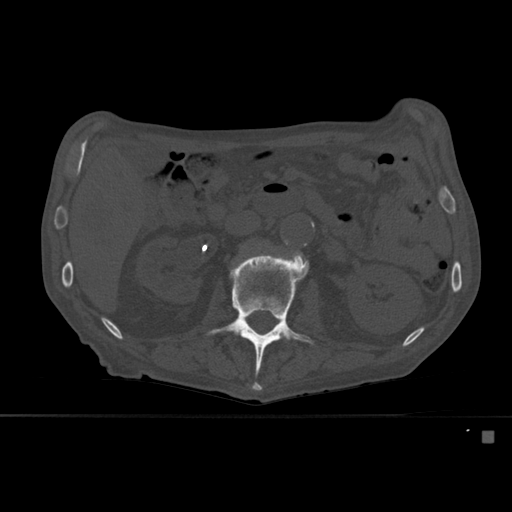
CT including the spine, one axial slice. Position 234 of 527 along the scan axis. Bone window (W 1800 / L 400 HU). 1.5 mm slice thickness. 512 × 512 image matrix, field of view 373 × 373 mm. Patient: male, 78 years. From the clinical record (not read from this slice): primary cancer: prostate.
Annotated regions visible in this slice (semi-automatic segmentation, software-assisted and operator-edited):
- L2 vertebra: bounding box [x1, y1, x2, y2] px = [206, 251, 315, 391]